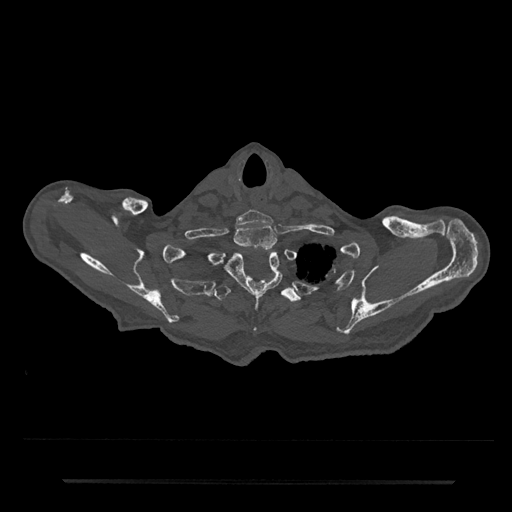
CT including the spine, one axial slice; position 695 of 797 along the scan axis; reconstruction kernel Br40s/3; 120 kVp; bone window (W 1800 / L 400 HU); 512 × 512 image matrix. Patient: male, 74 years. Case-level facts recorded for this patient, not image findings: primary cancer: prostate.
Outlined on this slice (semi-automatic segmentation, software-assisted and operator-edited):
- T1 vertebra: bounding box <234,225,277,250> (left, top, right, bottom; pixels)
- T2 vertebra: <219,250,283,301>
- T3 vertebra: <214,272,301,303>